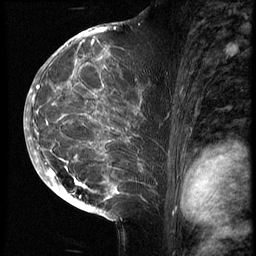
Breast MRI (dynamic contrast-enhanced), one sagittal slice; slice 37 of 70 in the series (ordered by position); 3 images stored at this slice position (order not interpretable as contrast timing); 1.5 T; TE 4.2 ms, TR 9 ms; 2.5 mm slice thickness; 256 × 256 image matrix, field of view 180 × 180 mm. Patient: female, 28 years. From the clinical record (not read from this slice): setting: breast cancer imaged before/during neoadjuvant chemotherapy.
Outlined on this slice (semi-automatic segmentation, software-assisted and operator-edited):
- analysis volume of interest (the breast-tissue region the enhancement analysis was run in; not a lesion): bounding box [x1, y1, x2, y2] px = [43, 42, 163, 215]
- tumour enhancement mask (voxels above the 140 % enhancement threshold inside the analysis volume of interest): [46, 42, 129, 203]